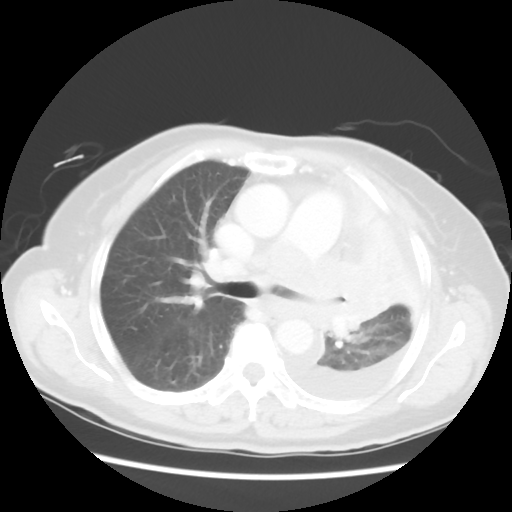
Chest CT, one axial slice; slice 34 of 52 in the series (ordered by position); lung window (W 1500 / L -600 HU); 5 mm slice thickness; 512 × 512 image matrix, field of view 336 × 336 mm. Female patient, age 72 years. Case-level facts recorded for this patient, not image findings: clinical TNM (as recorded): T4 N3 M1b.
Outlined on this slice (bounding box drawn by a radiologist):
- lung tumour (recorded histology: large cell carcinoma): bounding box [x1, y1, x2, y2] px = [311, 248, 388, 346]